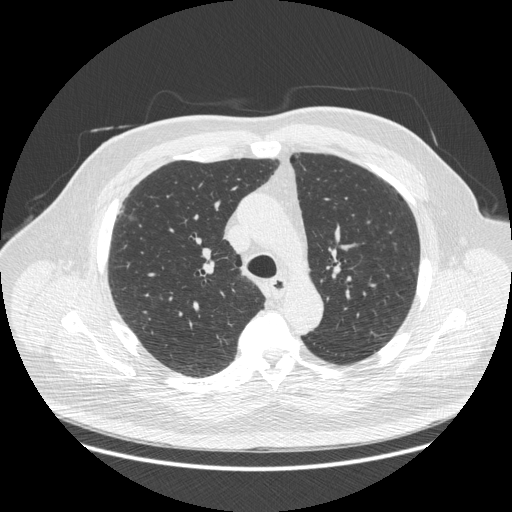
Chest CT (low-dose screening protocol), one axial image. Baseline screening round. Lung window (W 1500 / L -600 HU). 1.25 mm slice thickness. Standard (soft-tissue) reconstruction kernel (STANDARD). Slice 85 of 266 in the series. Male participant, aged 66 years at enrolment. Current smoker at enrolment.
Expert reader's lesion annotation, box from (x=110, y=203) to (x=145, y=231) px. Screening reader's record for this exam: no non-calcified nodule ≥4 mm recorded. Lung cancer was diagnosed 742 days after this screen (after the third annual screen): non-small cell carcinoma, right upper lobe, stage IV (AJCC 6th edition), 50 mm at pathology.